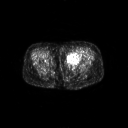
FDG PET of an extremity soft-tissue mass (from a PET/CT study), one axial slice. Slice 19 of 267 in the series (ordered by position). 3.27 mm slice thickness. 128 × 128 image matrix, field of view 700 × 700 mm. Female patient, age 47 years. From the clinical record (not read from this slice): histological type: myxofibrosarcoma; grade: intermediate; site of the primary tumour: left thigh.
Annotated regions visible in this slice (expert contour drawn on MRI and transferred to this co-registered scan by the dataset authors):
- gross tumour volume including surrounding oedema: box from (x=66, y=52) to (x=81, y=64) px
- gross tumour volume (mass): (x=67, y=52)–(x=81, y=64)